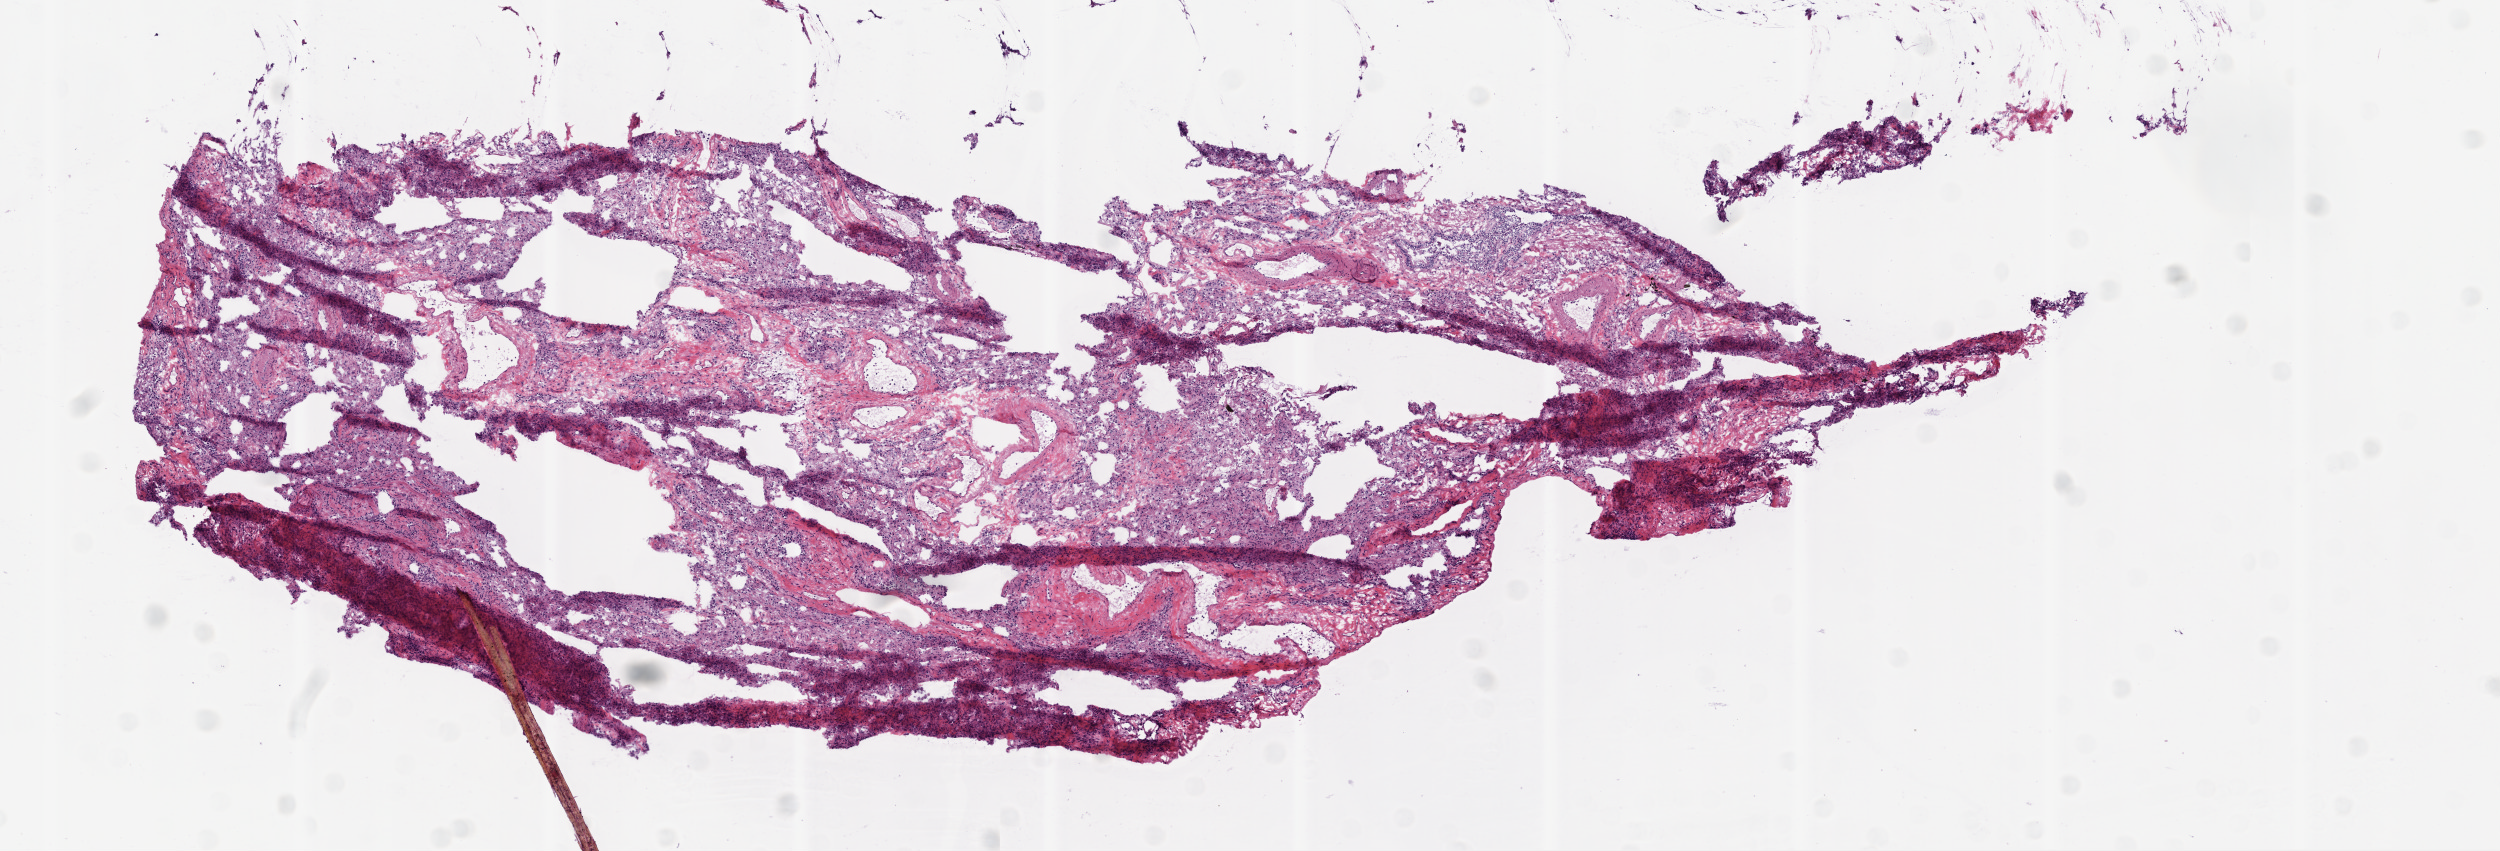
Hematoxylin and eosin (H&E) stained whole-slide image — low-resolution overview of the scanned area, about 10.0 x 3.4 mm (slide scanned at 20x), frozen section from the top of the tissue portion, sample: solid tissue normal (non-tumour tissue), lung. Male patient; age at initial diagnosis 73 years.
This section: solid tissue normal (non-tumour) sample from the same patient. Patient diagnosis: Squamous cell carcinoma, NOS (lower lobe, lung).